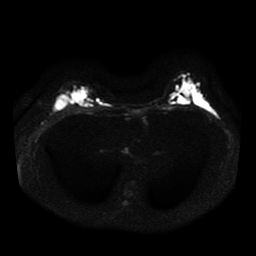
Breast MRI, one axial slice; position 27 of 41 along the scan axis; diffusion-weighted series; image 2 of 4 stored at this slice position (different b-values; order by instance number); 1.5 T; 5 mm slice thickness; 256 × 256 image matrix, field of view 330 × 330 mm. Female patient.
Structures marked on this image (expert manual segmentation):
- tumour on diffusion-weighted imaging: box from (x=54, y=95) to (x=66, y=111) px